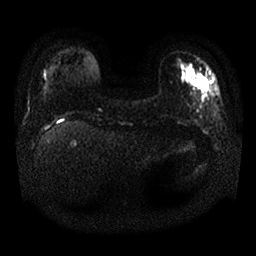
Breast MRI, one axial slice. Position 4 of 25 along the scan axis. Diffusion-weighted series; image 2 of 4 stored at this slice position (different b-values; order by instance number). 1.5 T. 4 mm slice thickness. 256 × 256 image matrix, field of view 340 × 340 mm. Female patient.
Structures marked on this image (manually delineated by an expert):
- tumour on diffusion-weighted imaging: box from (x=187, y=68) to (x=213, y=94) px